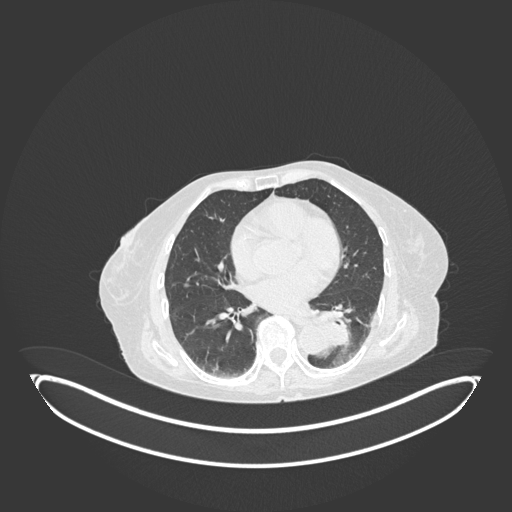
Chest CT, one axial slice; position 48 of 189 along the scan axis; 120 kVp; lung window (W 1500 / L -600 HU); 1 mm slice thickness; 512 × 512 image matrix, field of view 500 × 500 mm. Patient: female, 82 years. From the clinical record (not read from this slice): clinical TNM (as recorded): T1b N0 M1.
Annotated regions visible in this slice (bounding box drawn by a radiologist):
- lung tumour (recorded histology: adenocarcinoma): bounding box (x1, y1, x2, y2) in pixels: (311, 307, 359, 350)